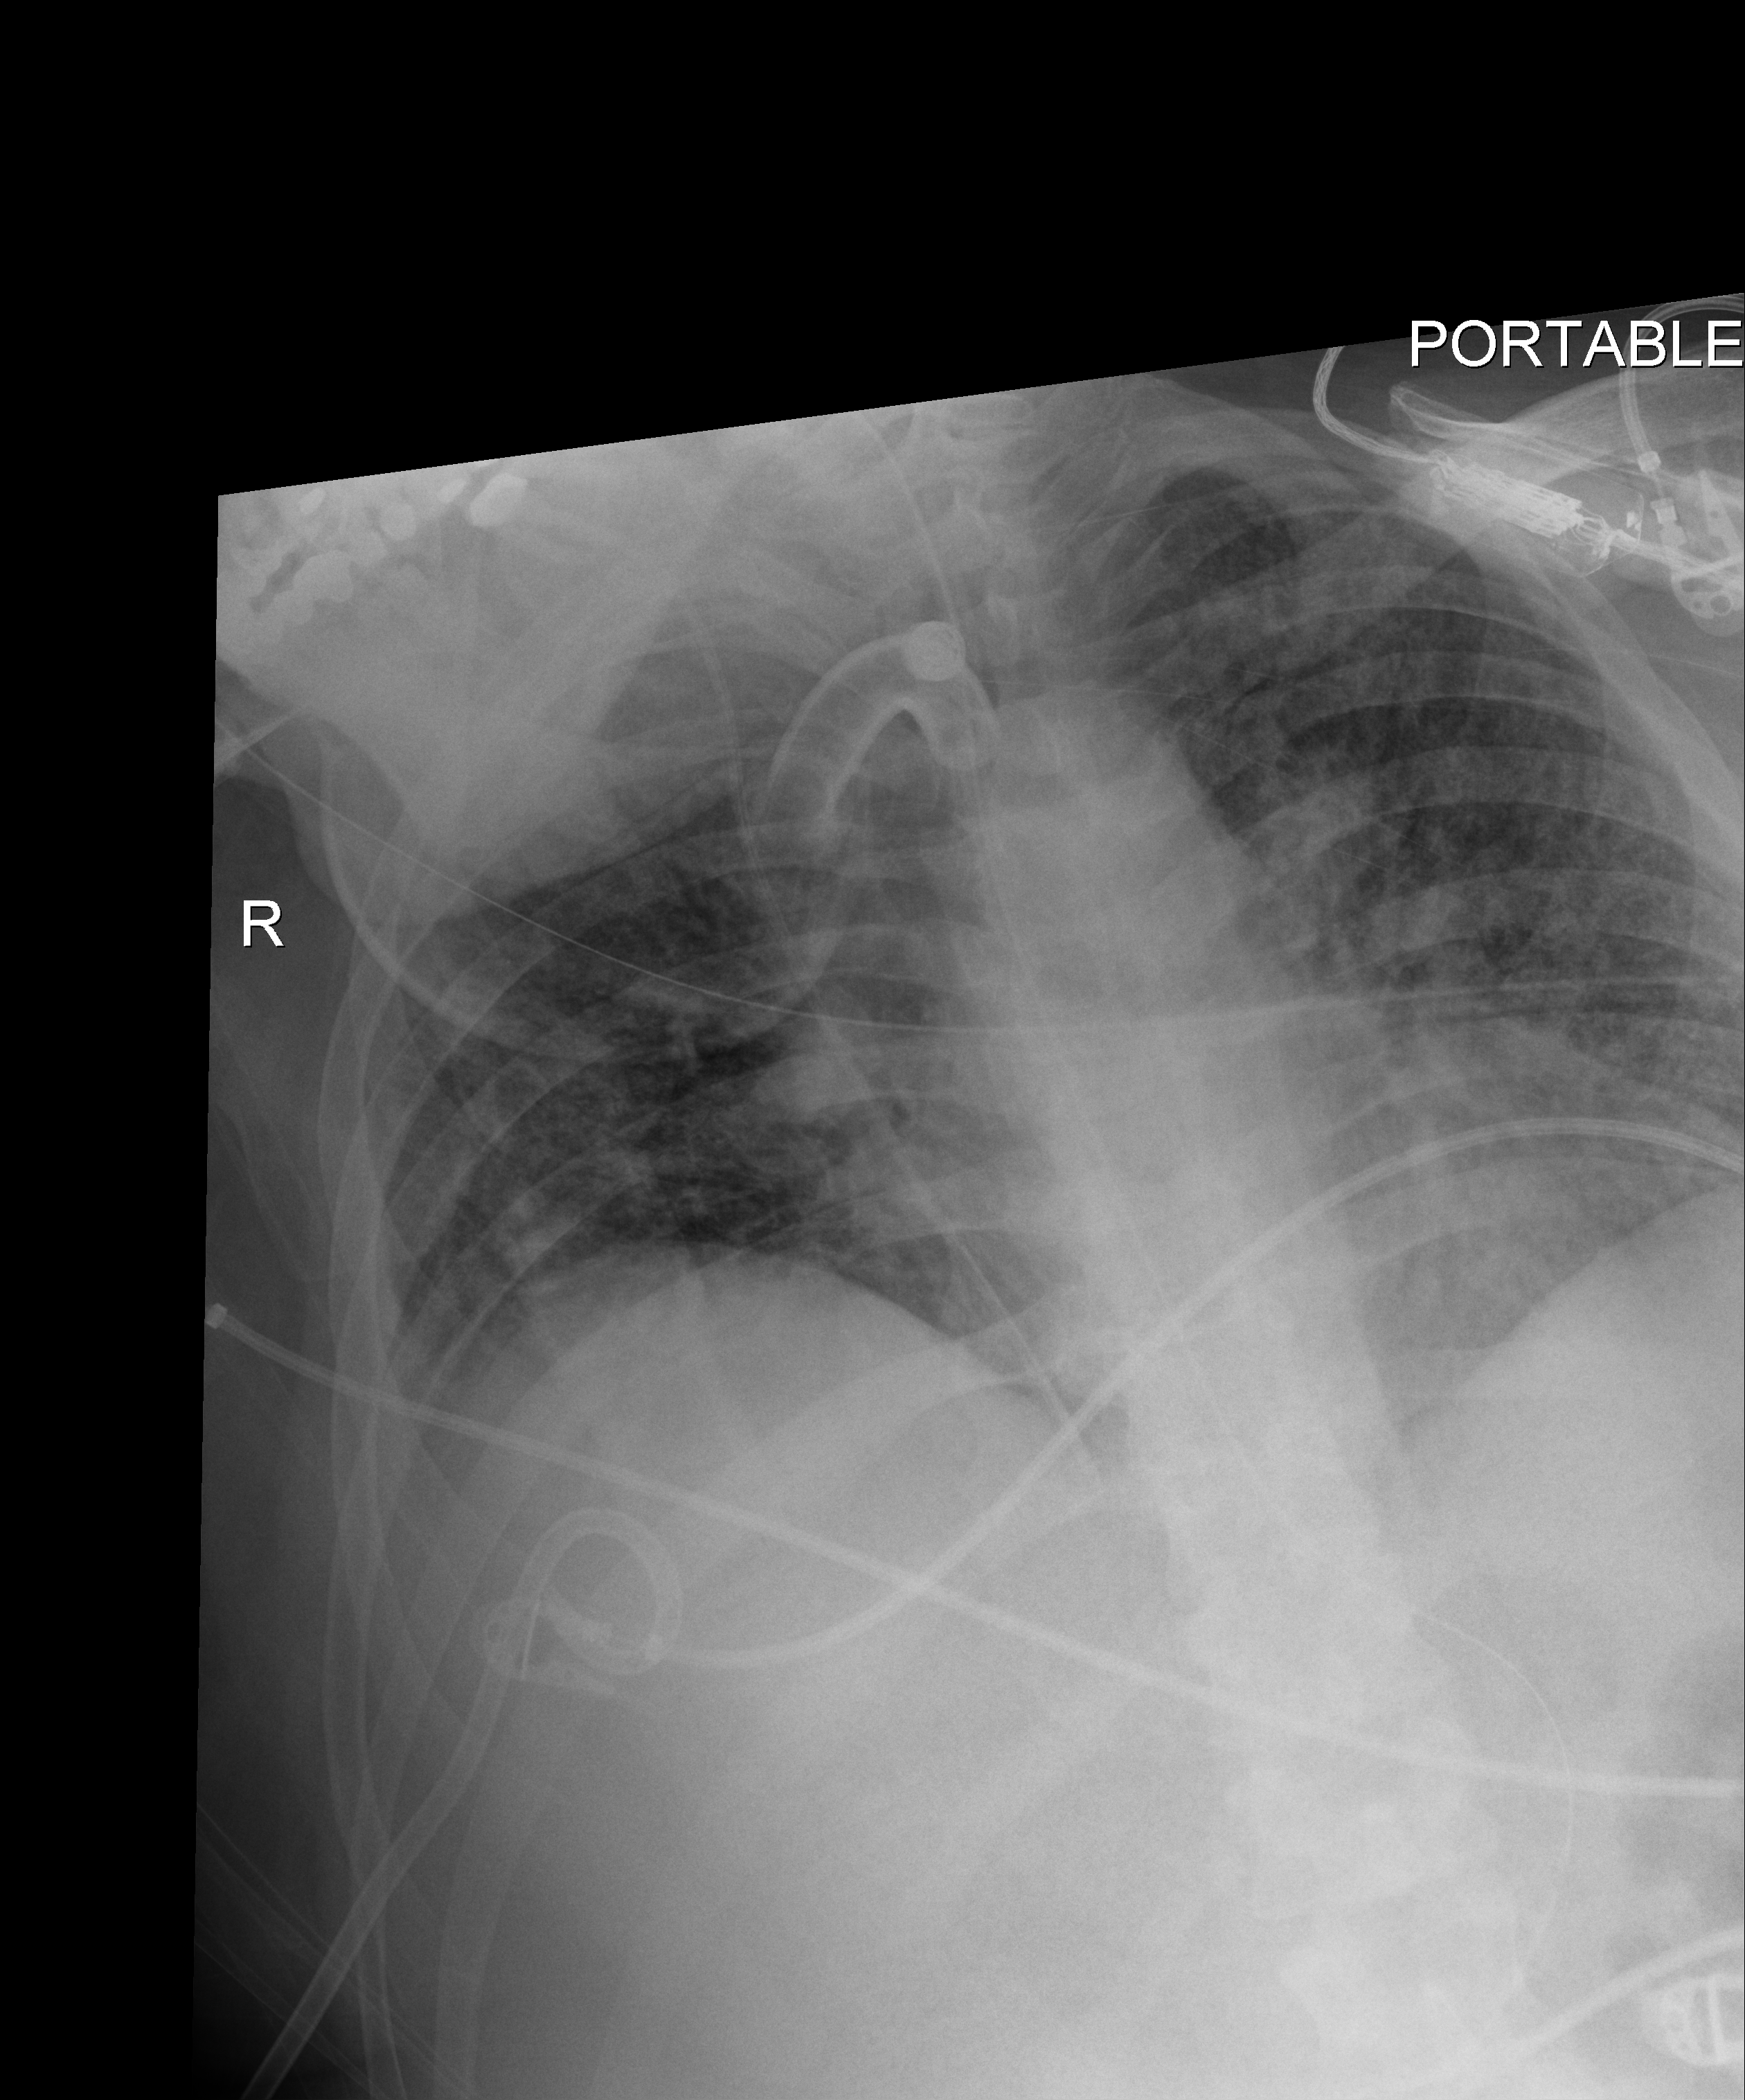
Chest X-ray (portable); anteroposterior (AP) projection. Male patient hospitalised with COVID-19, age 18–59 years.
From the hospital-stay record, not from the radiograph (when in the stay this image was taken is not recorded): admitted to intensive care during this hospital stay: yes; mechanically ventilated during this hospital stay: yes; hypertension (admission record): yes.